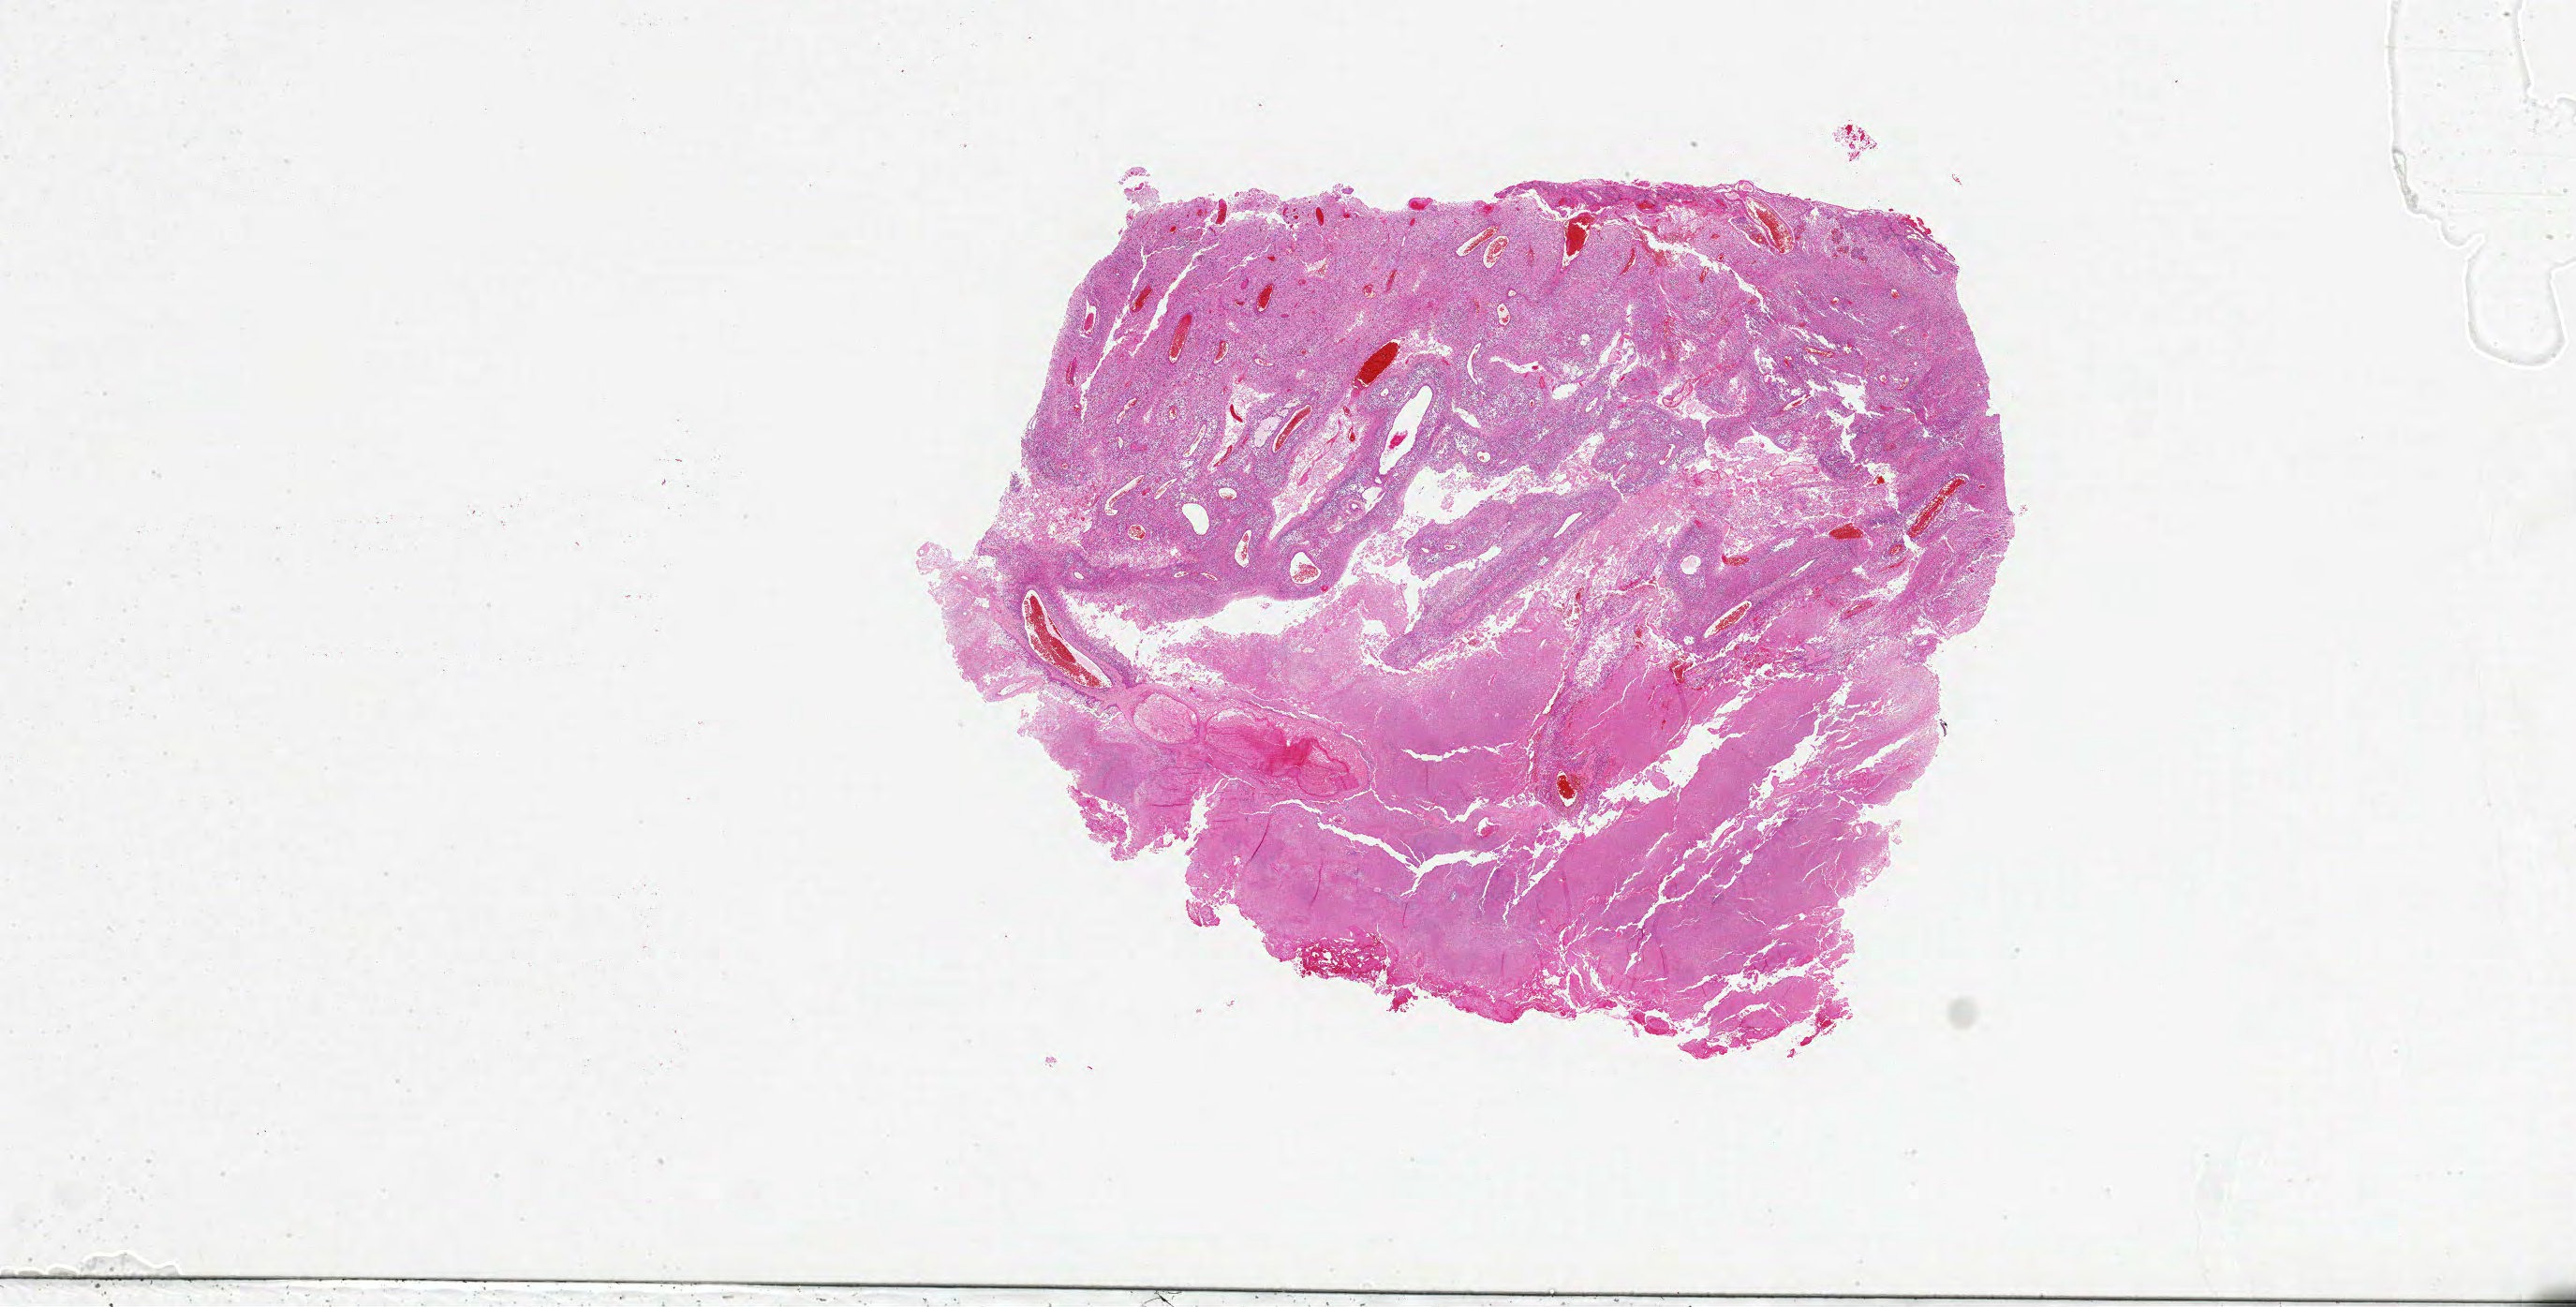
Digitized H&E-stained tissue section (whole slide), low-resolution overview of the scanned area, about 44.0 x 22.3 mm. Formalin-fixed paraffin-embedded (FFPE) diagnostic section. Sample: primary tumour, brain. Female, age 68 years at initial diagnosis.
Histologic diagnosis: Glioblastoma.